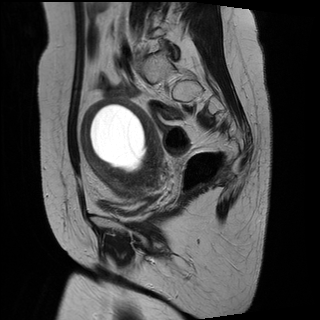
Pelvic MRI for cervical cancer, one sagittal slice; slice 20 of 29 in the series (ordered by position); T2-weighted; 1.5 T; TE 89 ms, TR 2930 ms; 4 mm slice thickness; 320 × 320 image matrix, field of view 260 × 260 mm. Patient: female, 49 years.
Annotated regions visible in this slice (manually delineated by an expert):
- uterus and cervix: bounding box (x1, y1, x2, y2) in pixels: (82, 96, 164, 198)